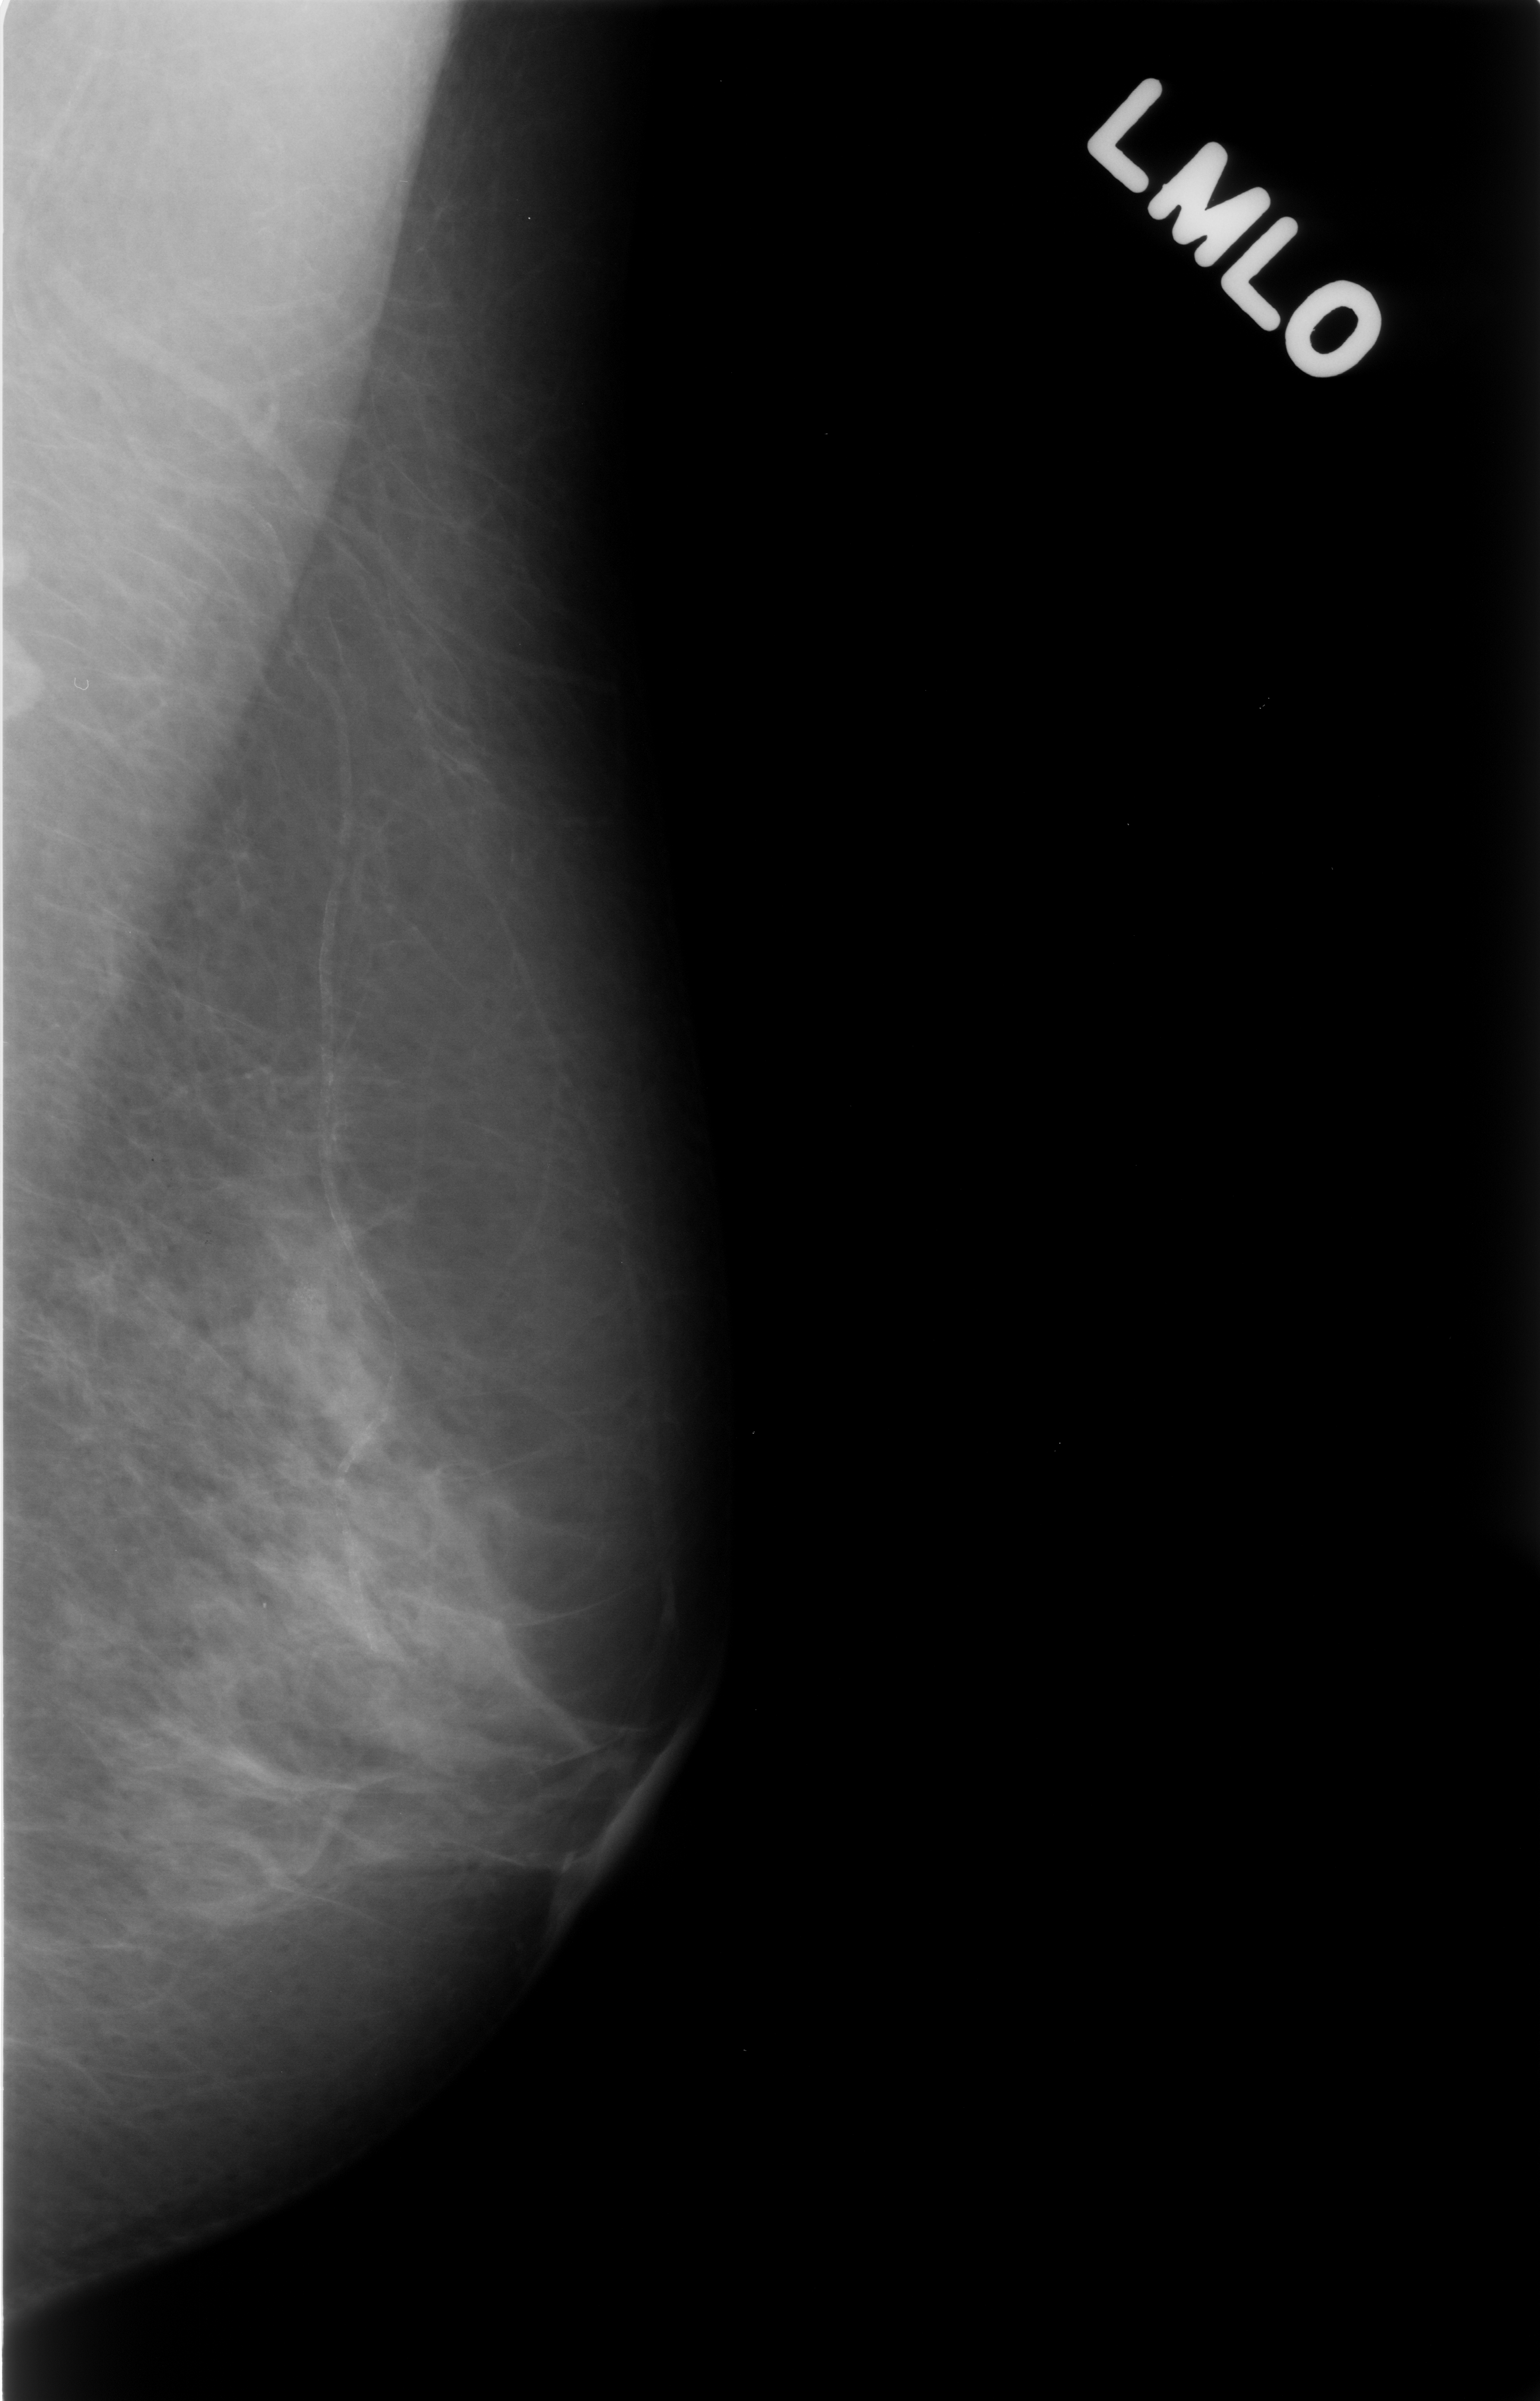
Digitized screen-film mammogram. Left breast. MLO view. Breast composition: scattered fibroglandular densities (BI-RADS density category 2 of 4). 1540 × 2401 image matrix.
Marked abnormalities (boxes around the expert regions of interest):
- calcifications, morphology amorphous, distribution clustered; BI-RADS assessment category 4; pathology (as recorded): benign: box from (x=241, y=1196) to (x=400, y=1405) px